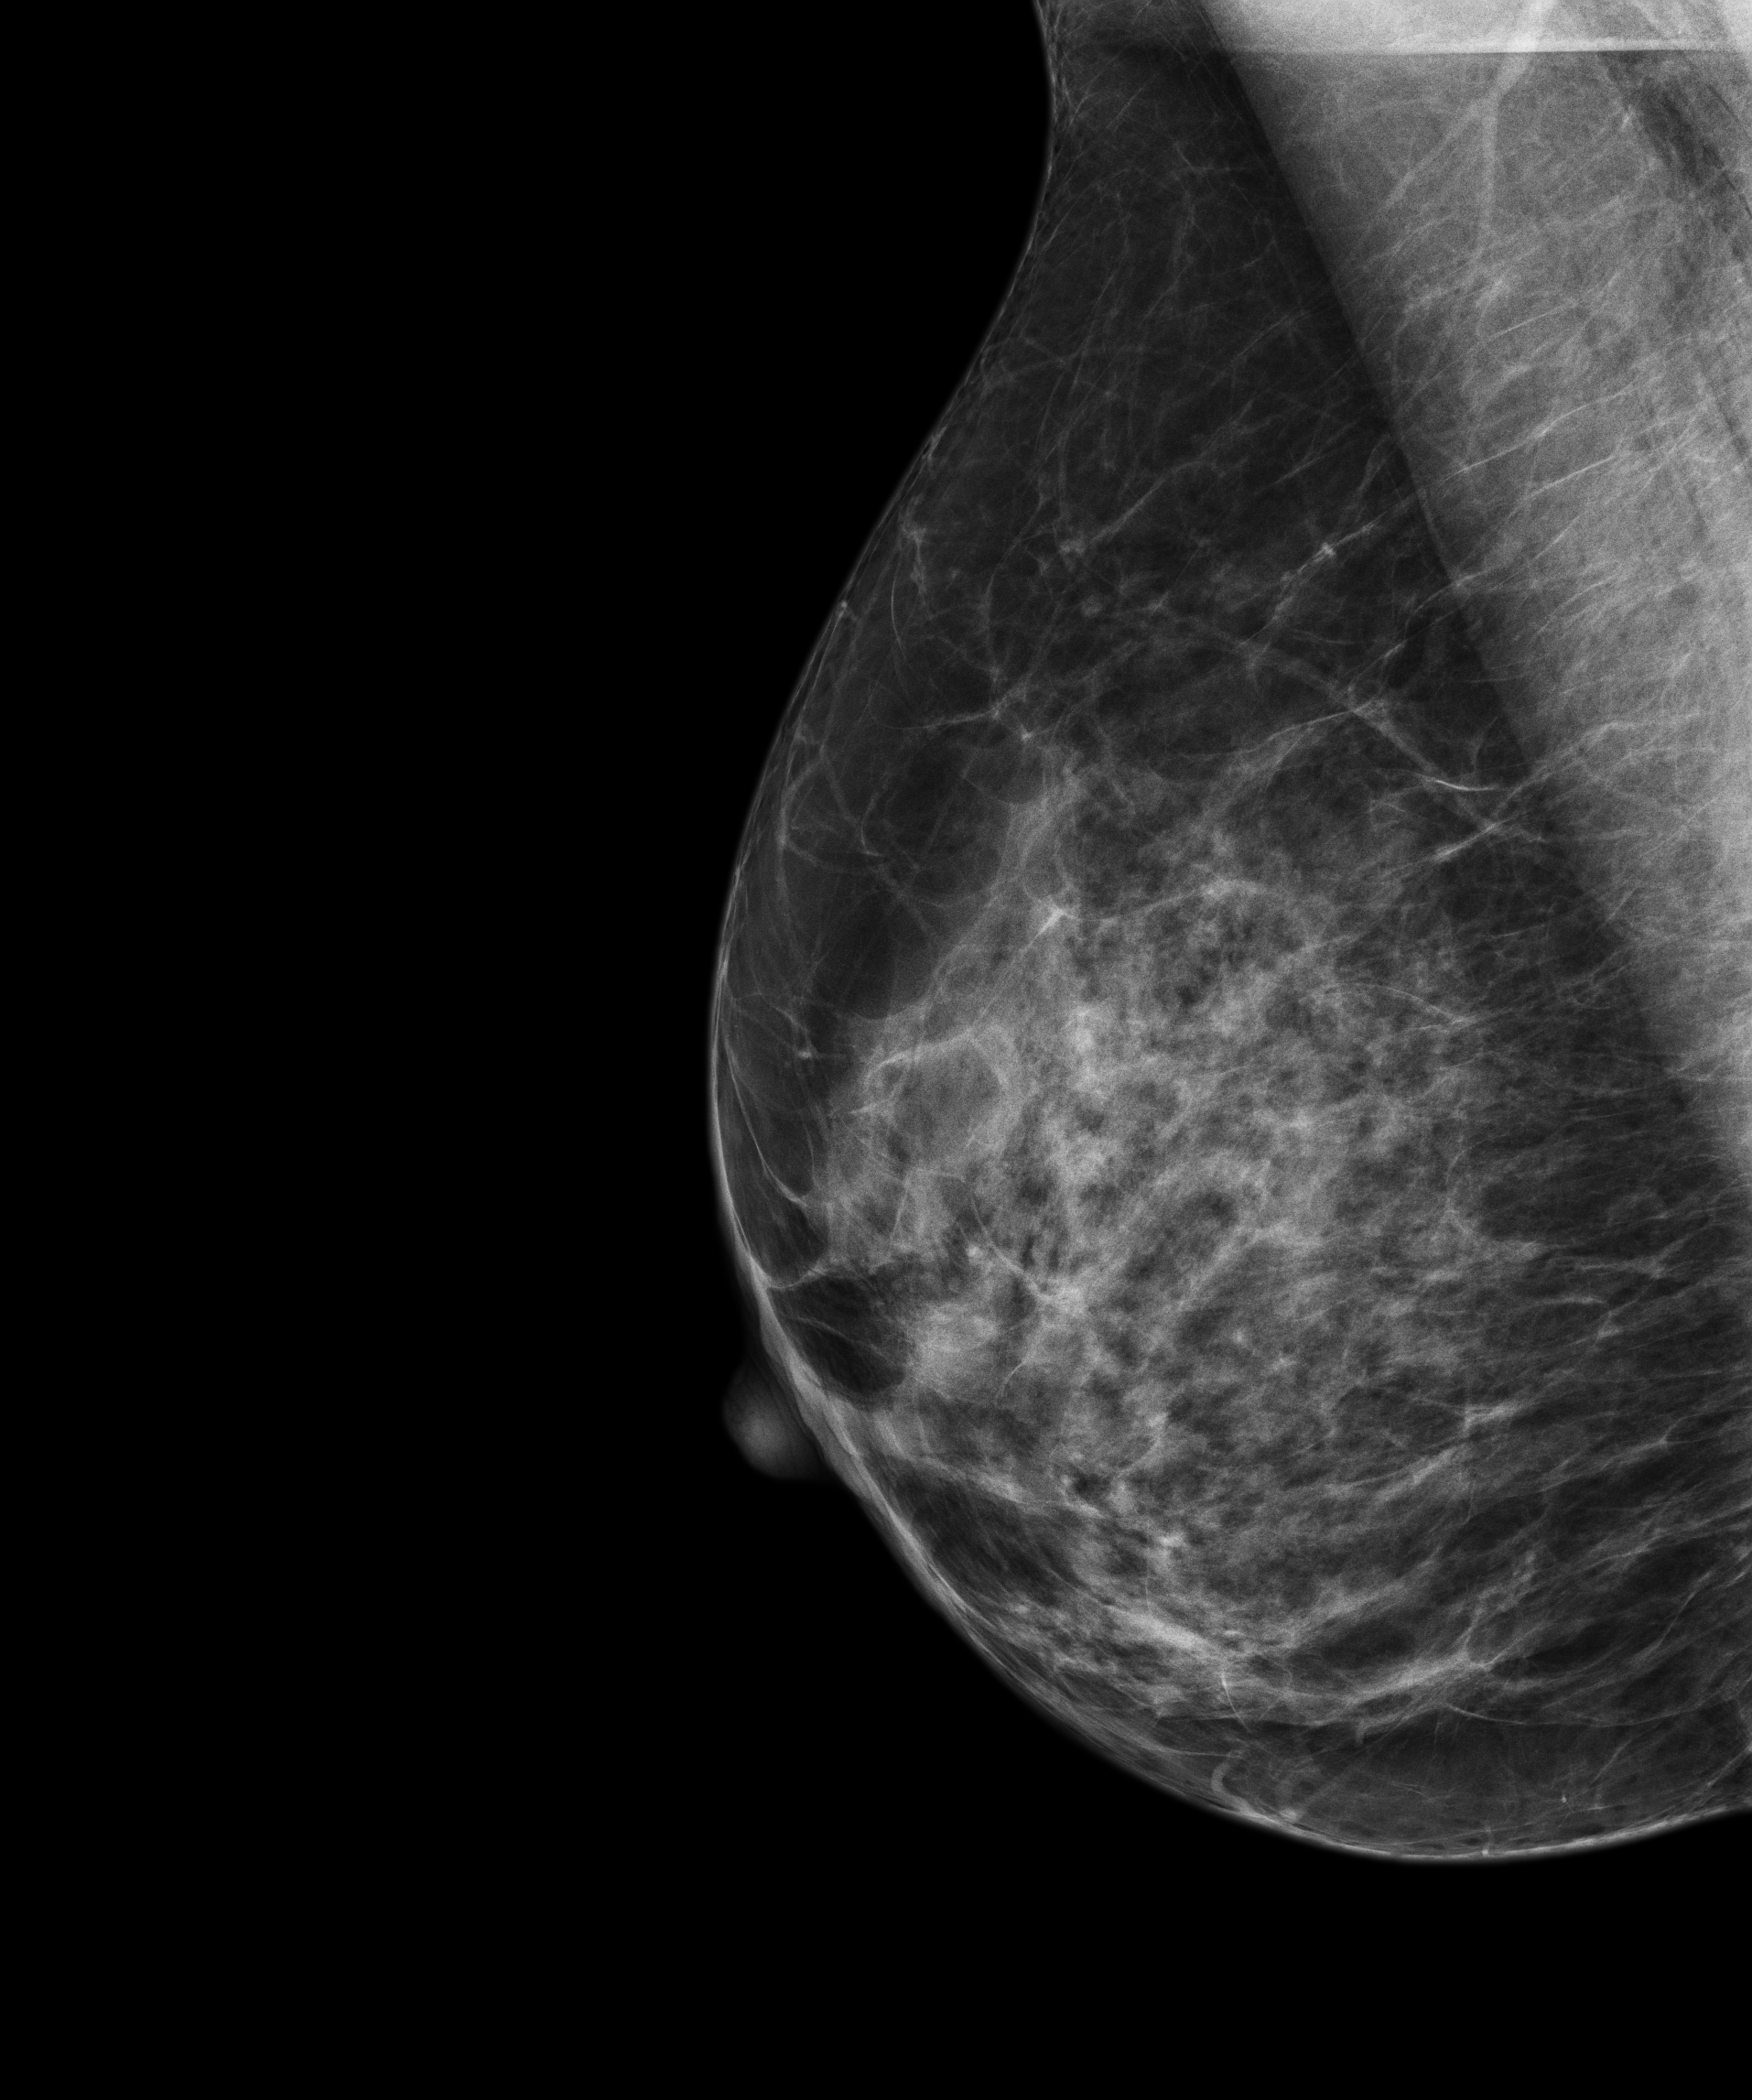
Screening examination. Patient: female, 53 years.
Image type: full-field digital mammogram. Breast: right. Projection: mediolateral oblique (MLO) view.